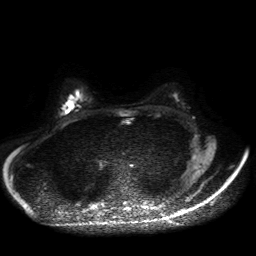
Breast MRI, one axial slice. Slice 29 of 50 in the series (ordered by position). Diffusion-weighted series; image 2 of 4 stored at this slice position (different b-values; order by instance number). 1.5 T. 256 × 256 image matrix. Female patient.
Structures marked on this image (manually delineated by an expert):
- tumour on diffusion-weighted imaging: box from (x=64, y=100) to (x=74, y=111) px